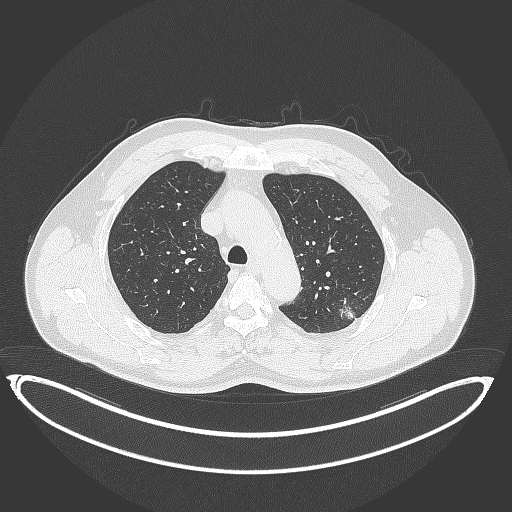
Chest CT, one axial slice; position 271 of 399 along the scan axis; lung window (W 1500 / L -600 HU); 512 × 512 image matrix, field of view 469 × 469 mm. Patient: male, 58 years. From the clinical record (not read from this slice): clinical TNM (as recorded): T1c N0 M0; histopathological grade: G1-2.
Annotated regions visible in this slice (rectangle marked by the reading radiologist):
- lung tumour (recorded histology: adenocarcinoma): box from (x=338, y=299) to (x=361, y=327) px